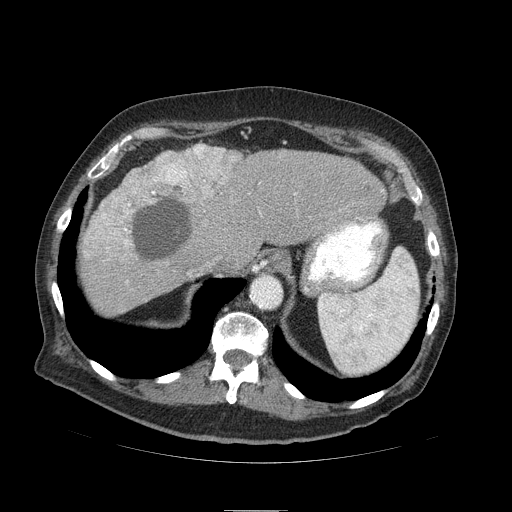
Contrast-enhanced abdominal CT (liver protocol), one axial slice. Slice 72 of 103 in the series (ordered by position). Reconstruction kernel STANDARD. 120 kVp. Soft-tissue window (W 400 / L 40 HU). 512 × 512 image matrix. From the clinical record (not read from this slice): diagnosis: hepatocellular carcinoma (patient treated with transarterial chemoembolisation; whether this scan precedes or follows treatment is not stated here); TNM stage (as recorded): Stage-IIIA; Child-Pugh class: B; tumour differentiation: well differentiated; tumour size: 13 cm.
Outlined on this slice (semi-automatically segmented with operator editing):
- liver parenchyma outside the tumour (the mass and vessels are separate outlines, so this box may not span the whole liver): bounding box <80,144,386,314> (left, top, right, bottom; pixels)
- mass: <86,147,243,261>